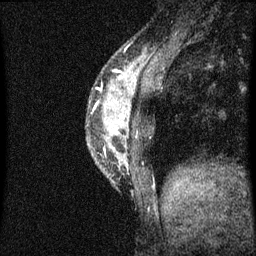
Breast MRI (dynamic contrast-enhanced), one sagittal slice; slice 16 of 60 in the series (ordered by position); dynamic contrast-enhanced series, image 2 of 3 at this slice position (ordered by acquisition); 1.5 T; TE 4.2 ms, TR 8 ms; 2 mm slice thickness; 256 × 256 image matrix, field of view 180 × 180 mm. Patient: female, 33 years.
Structures marked on this image (semi-automatic segmentation, software-assisted and operator-edited):
- analysis volume of interest (the breast-tissue region the enhancement analysis was run in; not a lesion): bounding box <89,58,151,191> (left, top, right, bottom; pixels)
- tumour enhancement mask (voxels above the 70 % enhancement threshold inside the analysis volume of interest): <120,78,126,119>